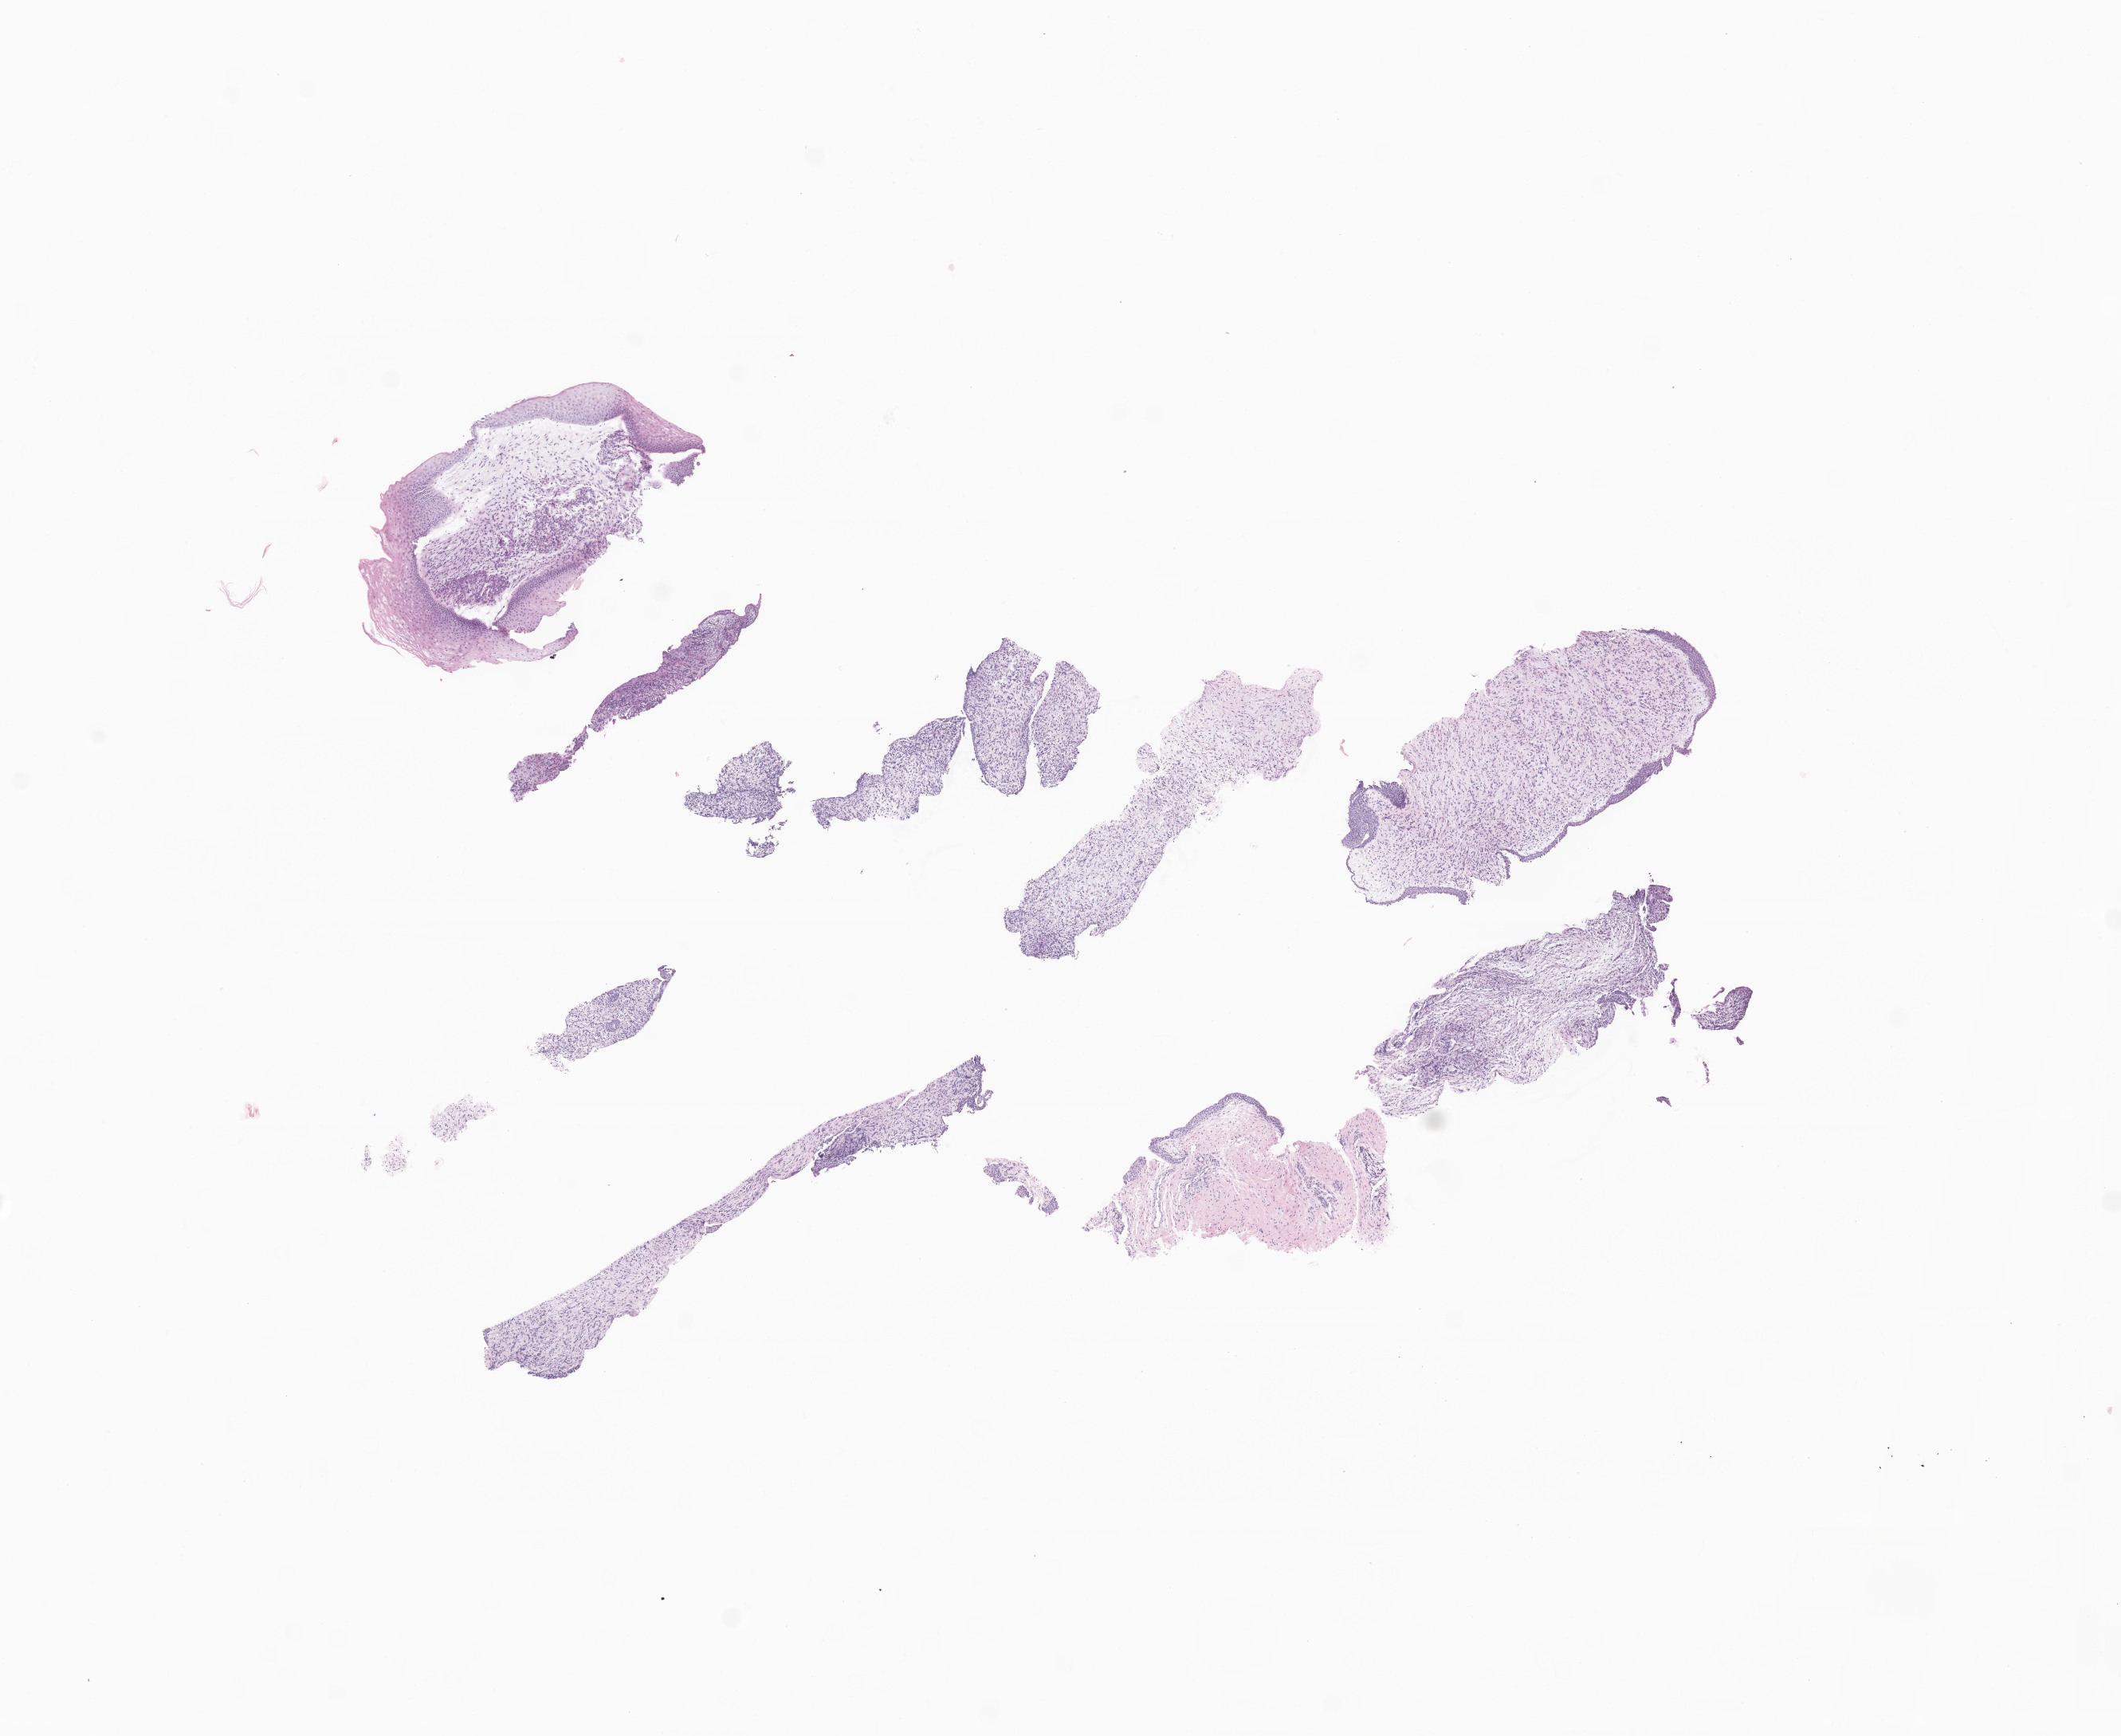
Haematoxylin and eosin whole-slide image of tumor tissue from the urinary bladder — whole scanned area (about 11.2 x 9.2 mm) shown as a low-resolution overview, formalin-fixed paraffin-embedded section. Male patient, age 47 months (3 years 11 months).
Diagnosis (ICD-O-3 morphology term): Embryonal rhabdomyosarcoma, NOS.